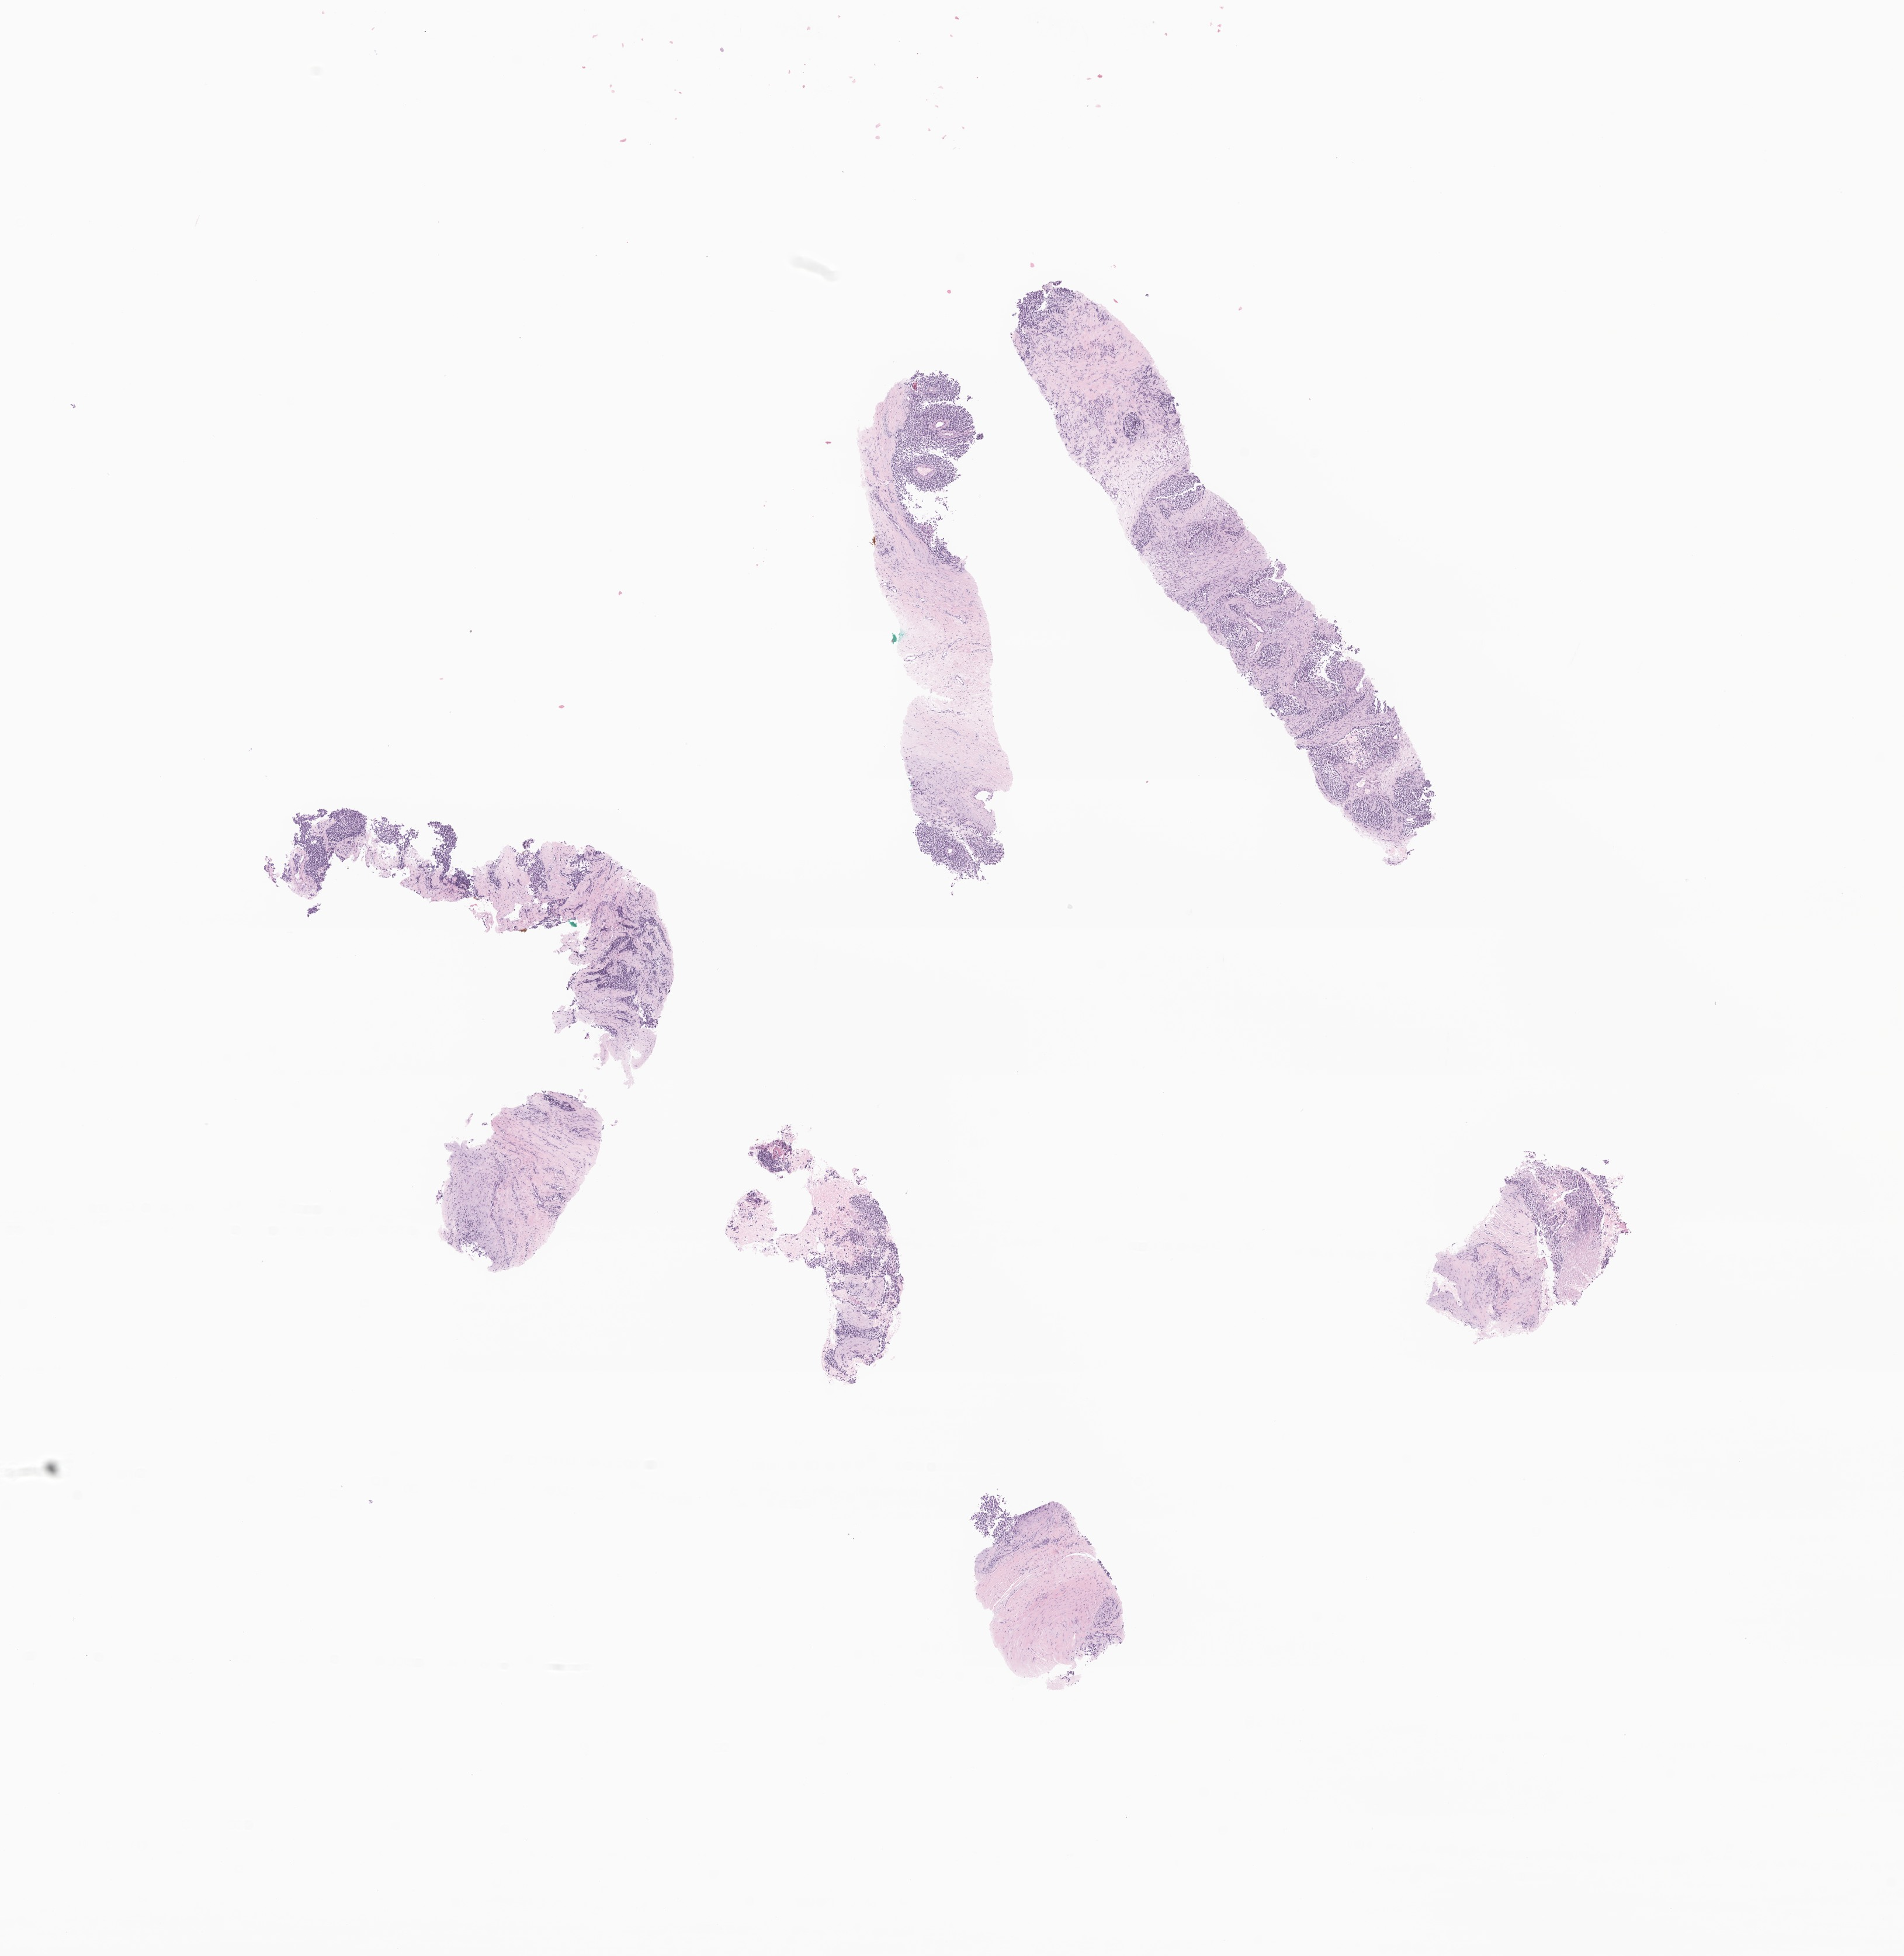
H&E whole-slide image of tumor tissue from the lower limb — whole scanned area (about 13.7 x 14.1 mm) shown as a low-resolution overview; formalin-fixed, paraffin-embedded (FFPE) tissue. Female patient, age 124 months (10 years 4 months).
* diagnosis (ICD-O-3 morphology term): Alveolar rhabdomyosarcoma